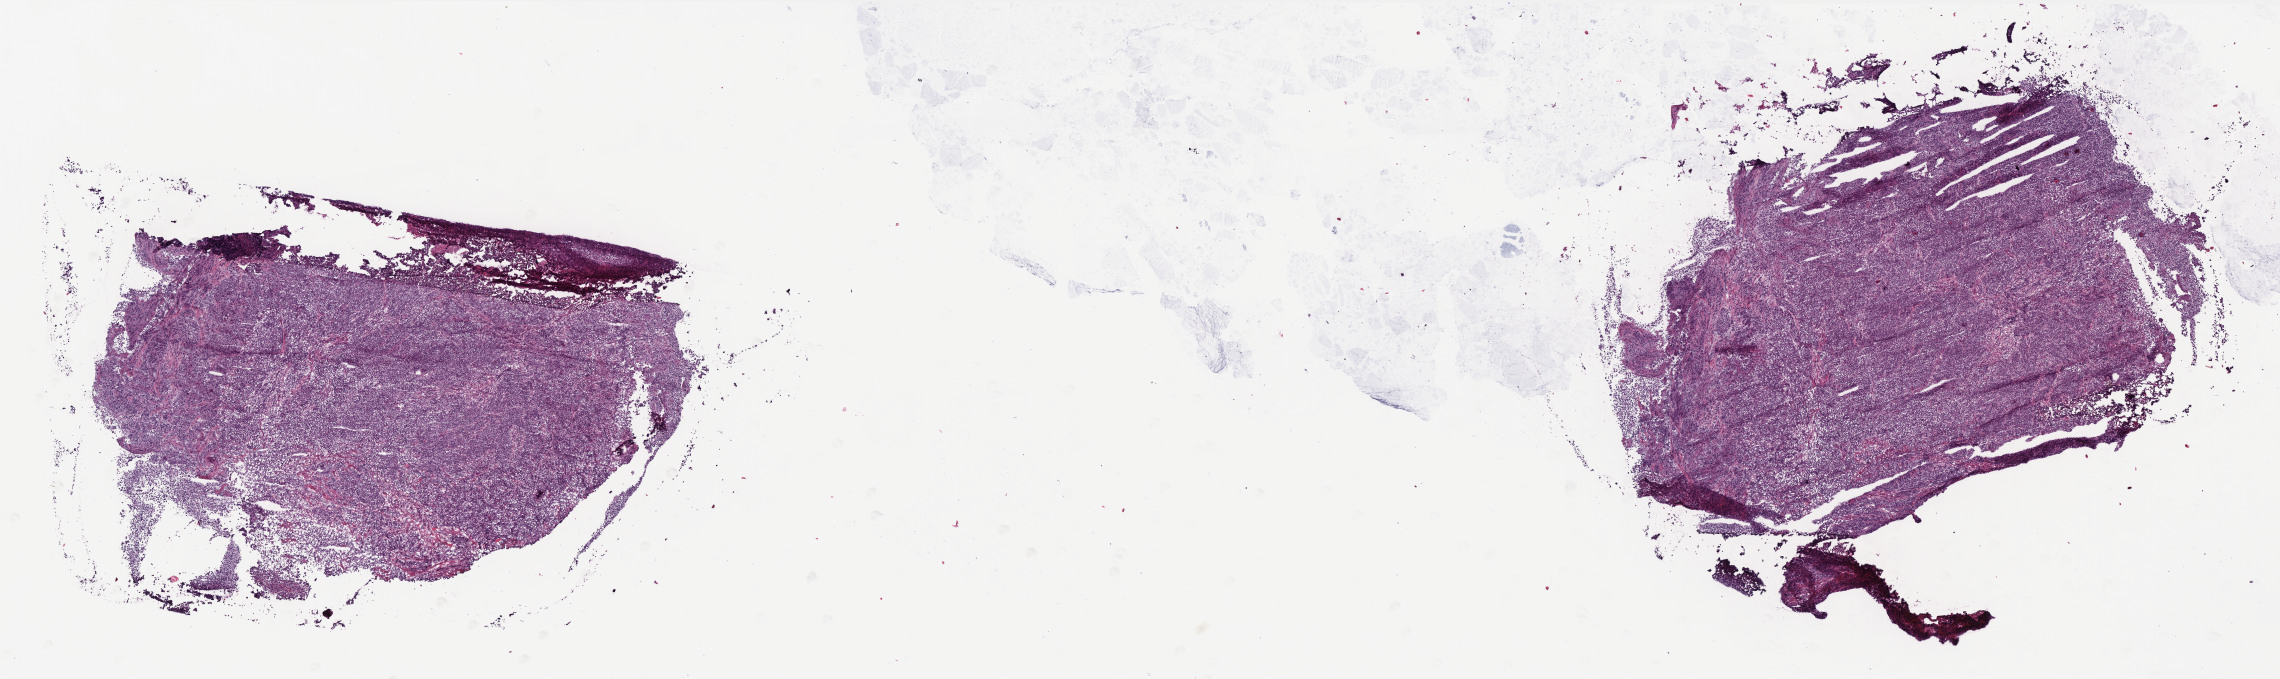
Digitized H&E-stained tissue section (whole slide) — whole scanned area (about 18.3 x 5.4 mm, slide scanned at 40x) shown as a low-resolution overview; frozen section from the top of the tissue portion; sample: primary tumour, colon. Female patient; age at initial diagnosis 64 years. Composition of this section per pathologist review: tumour cells 90%, tumour nuclei 95%, normal cells 0%, stromal cells 8%, necrosis 2%. Infiltration values recorded for this section: lymphocyte infiltration 1%, monocyte infiltration 1%, neutrophil infiltration 2%.
AJCC pathologic stage: I (6th edition). Lymph nodes positive (case pathology): 0 of 27 examined. Pathologic diagnosis: Adenocarcinoma, NOS (cecum).